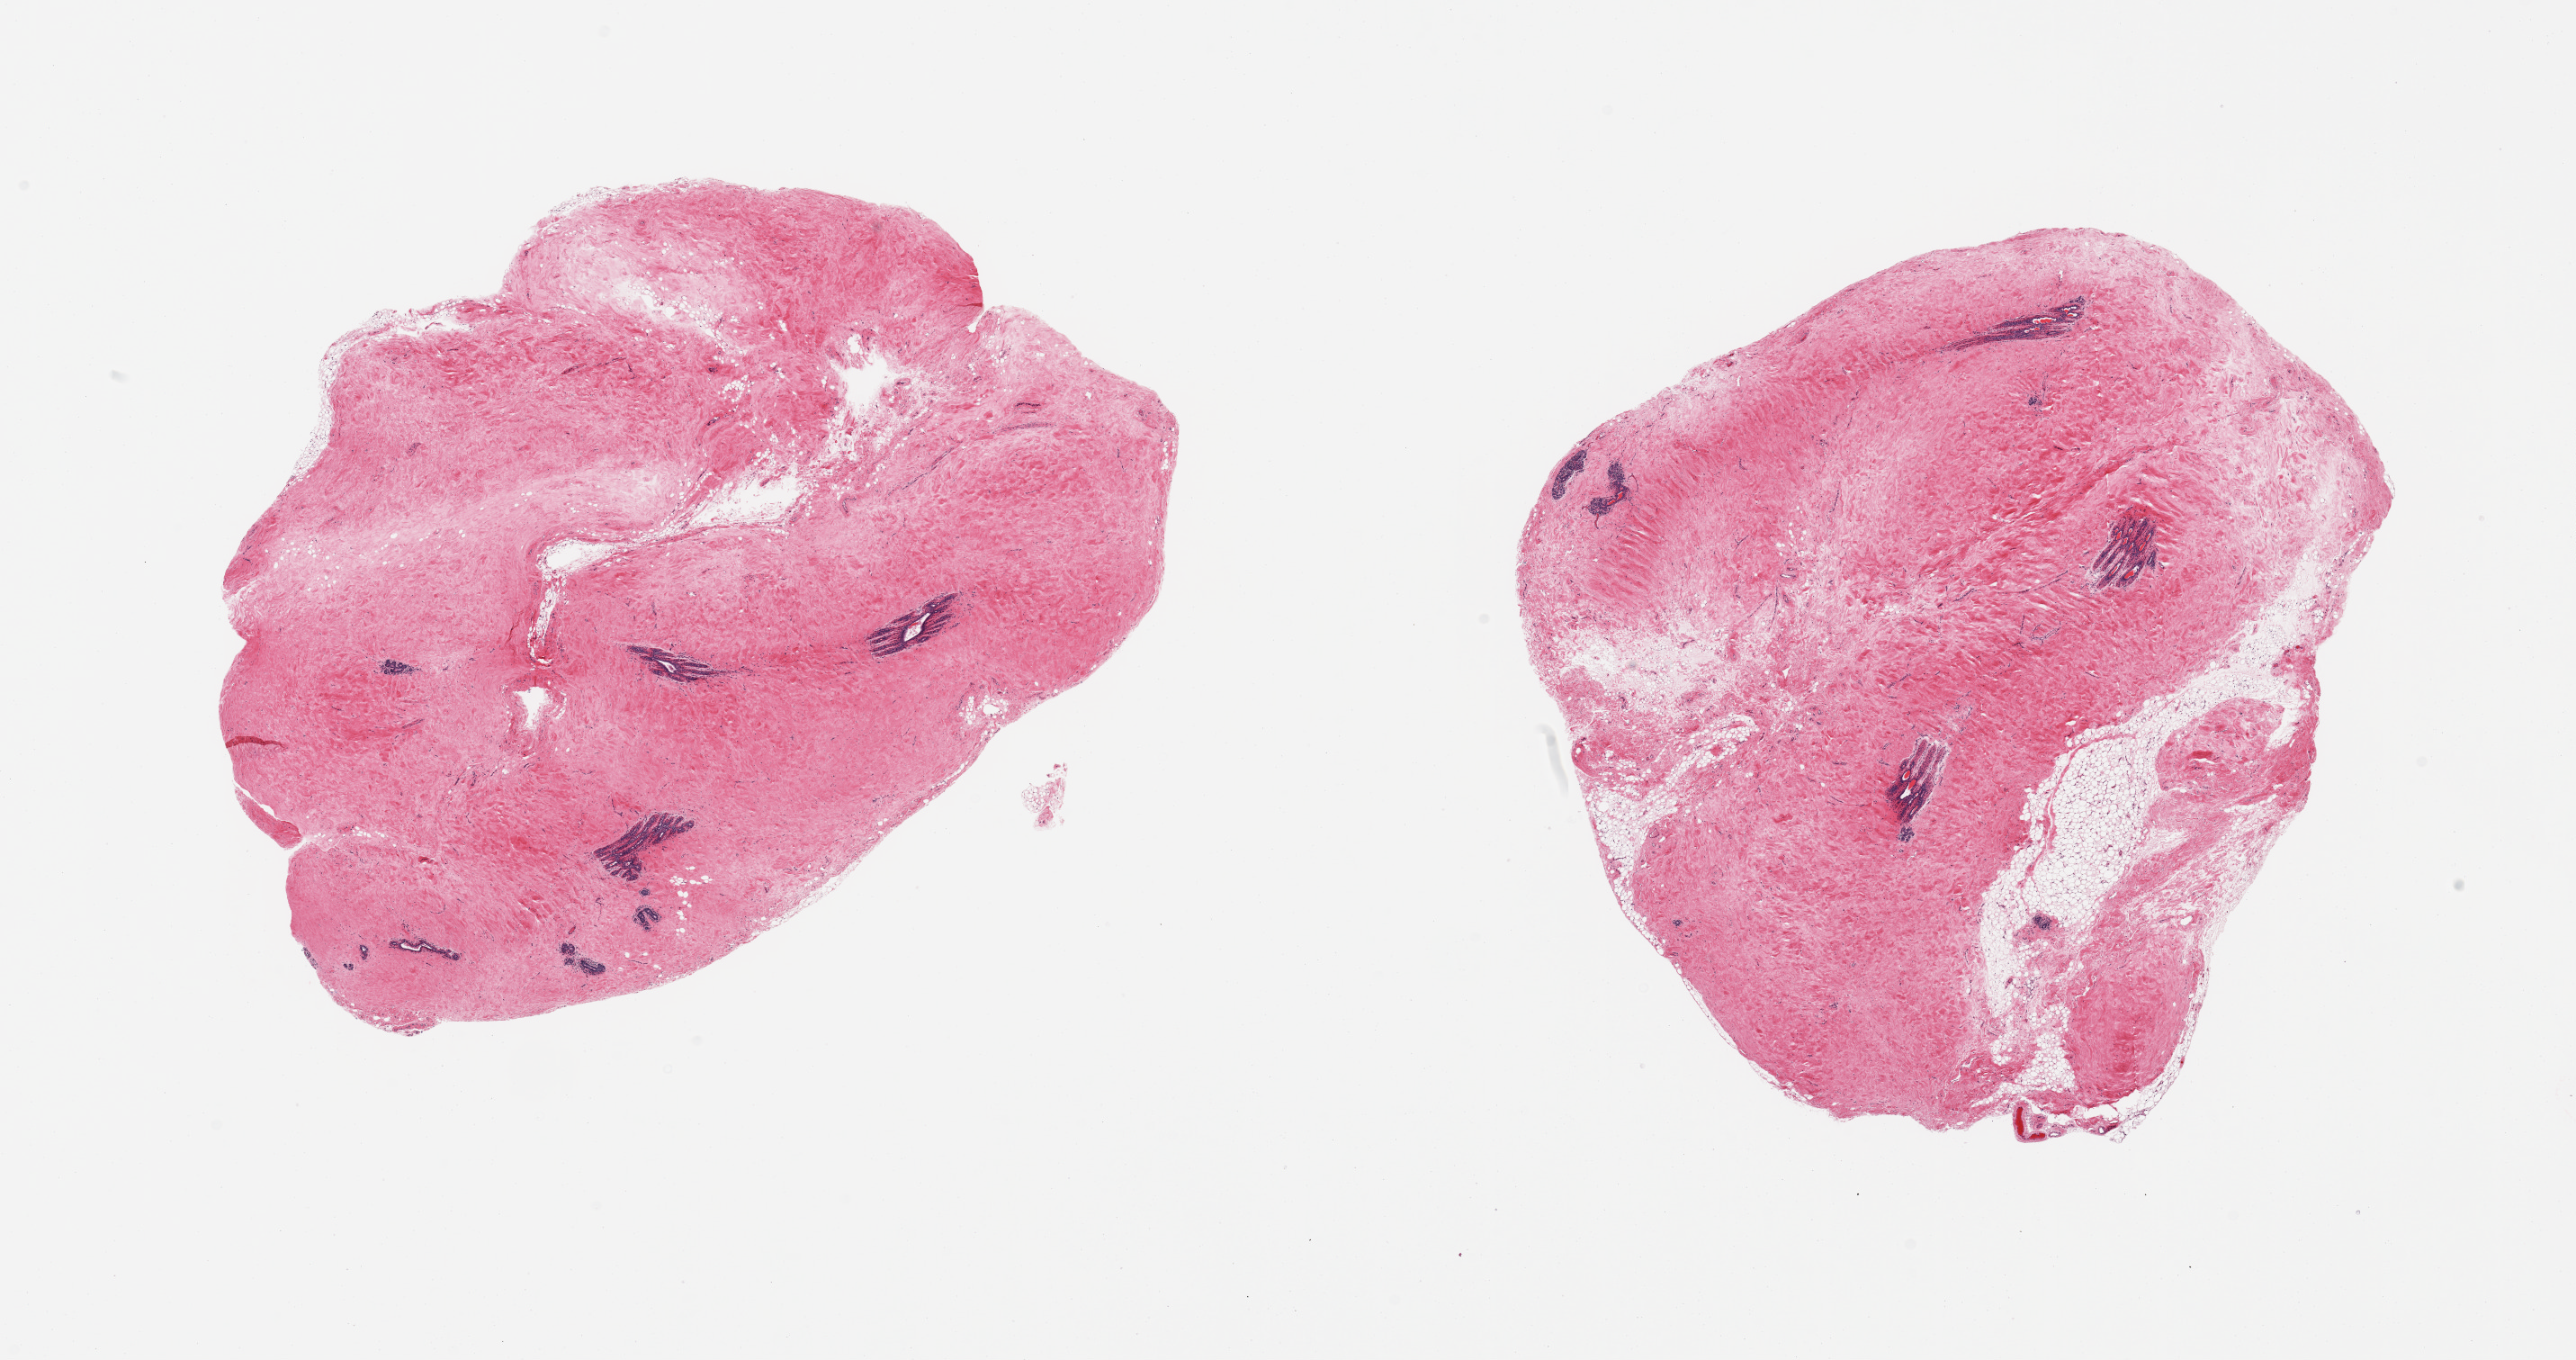
Digitized haematoxylin and eosin-stained section, whole scanned area (about 22.6 x 11.9 mm) shown as a low-resolution overview; PAXgene-fixed paraffin-embedded (PFPE) section; target tissue: breast; donor tissue sample.
Pathologist's review note for this sample: 2 pieces; lobular and ductal elements; mainly fibrous: 95% & 80%, remainder fat.